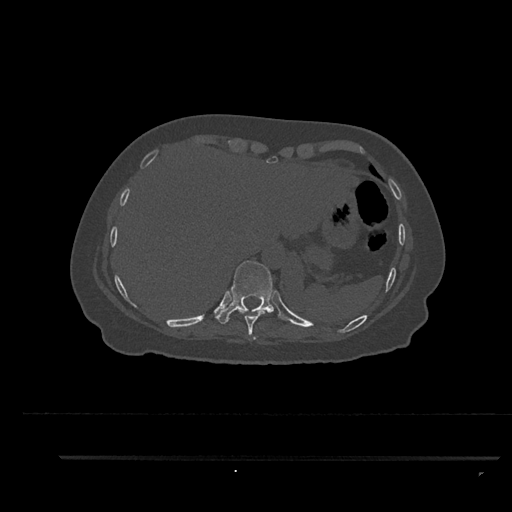
CT including the spine, one axial slice. Slice 385 of 797 in the series (ordered by position). 120 kVp. Bone window (W 1800 / L 400 HU). 0.5 mm slice thickness. 512 × 512 image matrix, field of view 408 × 408 mm. Patient: female, 44 years. Case-level facts recorded for this patient, not image findings: primary cancer: renal; vertebrae with lytic lesions (as recorded): L1.
Annotated regions visible in this slice (semi-automatic segmentation, software-assisted and operator-edited):
- T10 vertebra: box from (x=215, y=260) to (x=283, y=324) px
- T9 vertebra: (x=238, y=308)–(x=266, y=340)